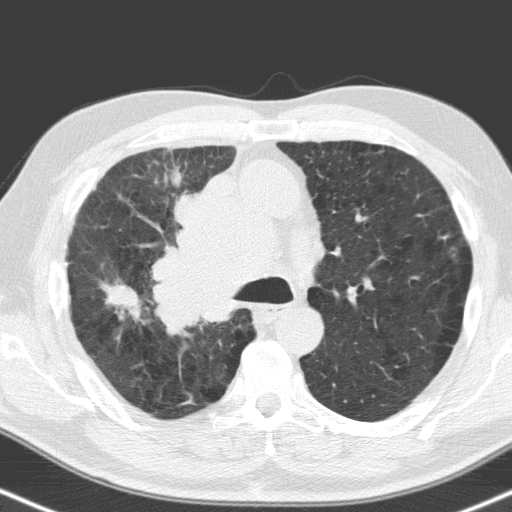
Low-dose screening chest CT, axial slice, first (baseline) screen, lung window (W 1500 / L -600 HU), 3.2 mm slice thickness, standard (soft-tissue) reconstruction kernel (C), slice 50 of 160 in the series. Male, age 71 years at enrolment.
• Lesion marked by an expert reader, box from (x=86, y=271) to (x=158, y=339) px.
• The screening reader recorded 2 non-calcified nodules or masses ≥4 mm on this exam (right upper lobe, right upper lobe); which of them this box marks is not recorded.
• Official screen result: positive, change unspecified: nodule(s) >= 4 mm or enlarging nodule(s), mass(es), or other non-specific abnormalities suspicious for lung cancer.
• Participant outcome: lung cancer diagnosed 31 days after this screen — small cell carcinoma, NOS, right upper lobe, stage IV (AJCC 6th edition), 40 mm at pathology.